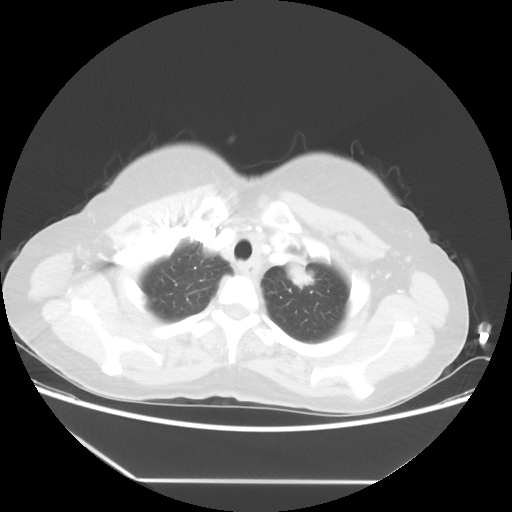
Chest CT, one axial slice; slice 46 of 52 in the series (ordered by position); reconstruction kernel STANDARD; 100 kVp; lung window (W 1500 / L -600 HU); 512 × 512 image matrix, field of view 390 × 390 mm. Female patient, age 50 years. Case-level facts recorded for this patient, not image findings: clinical TNM (as recorded): T2 N3 M0.
Annotated regions visible in this slice (rectangle marked by the reading radiologist):
- lung tumour (recorded histology: adenocarcinoma): box from (x=280, y=257) to (x=328, y=300) px